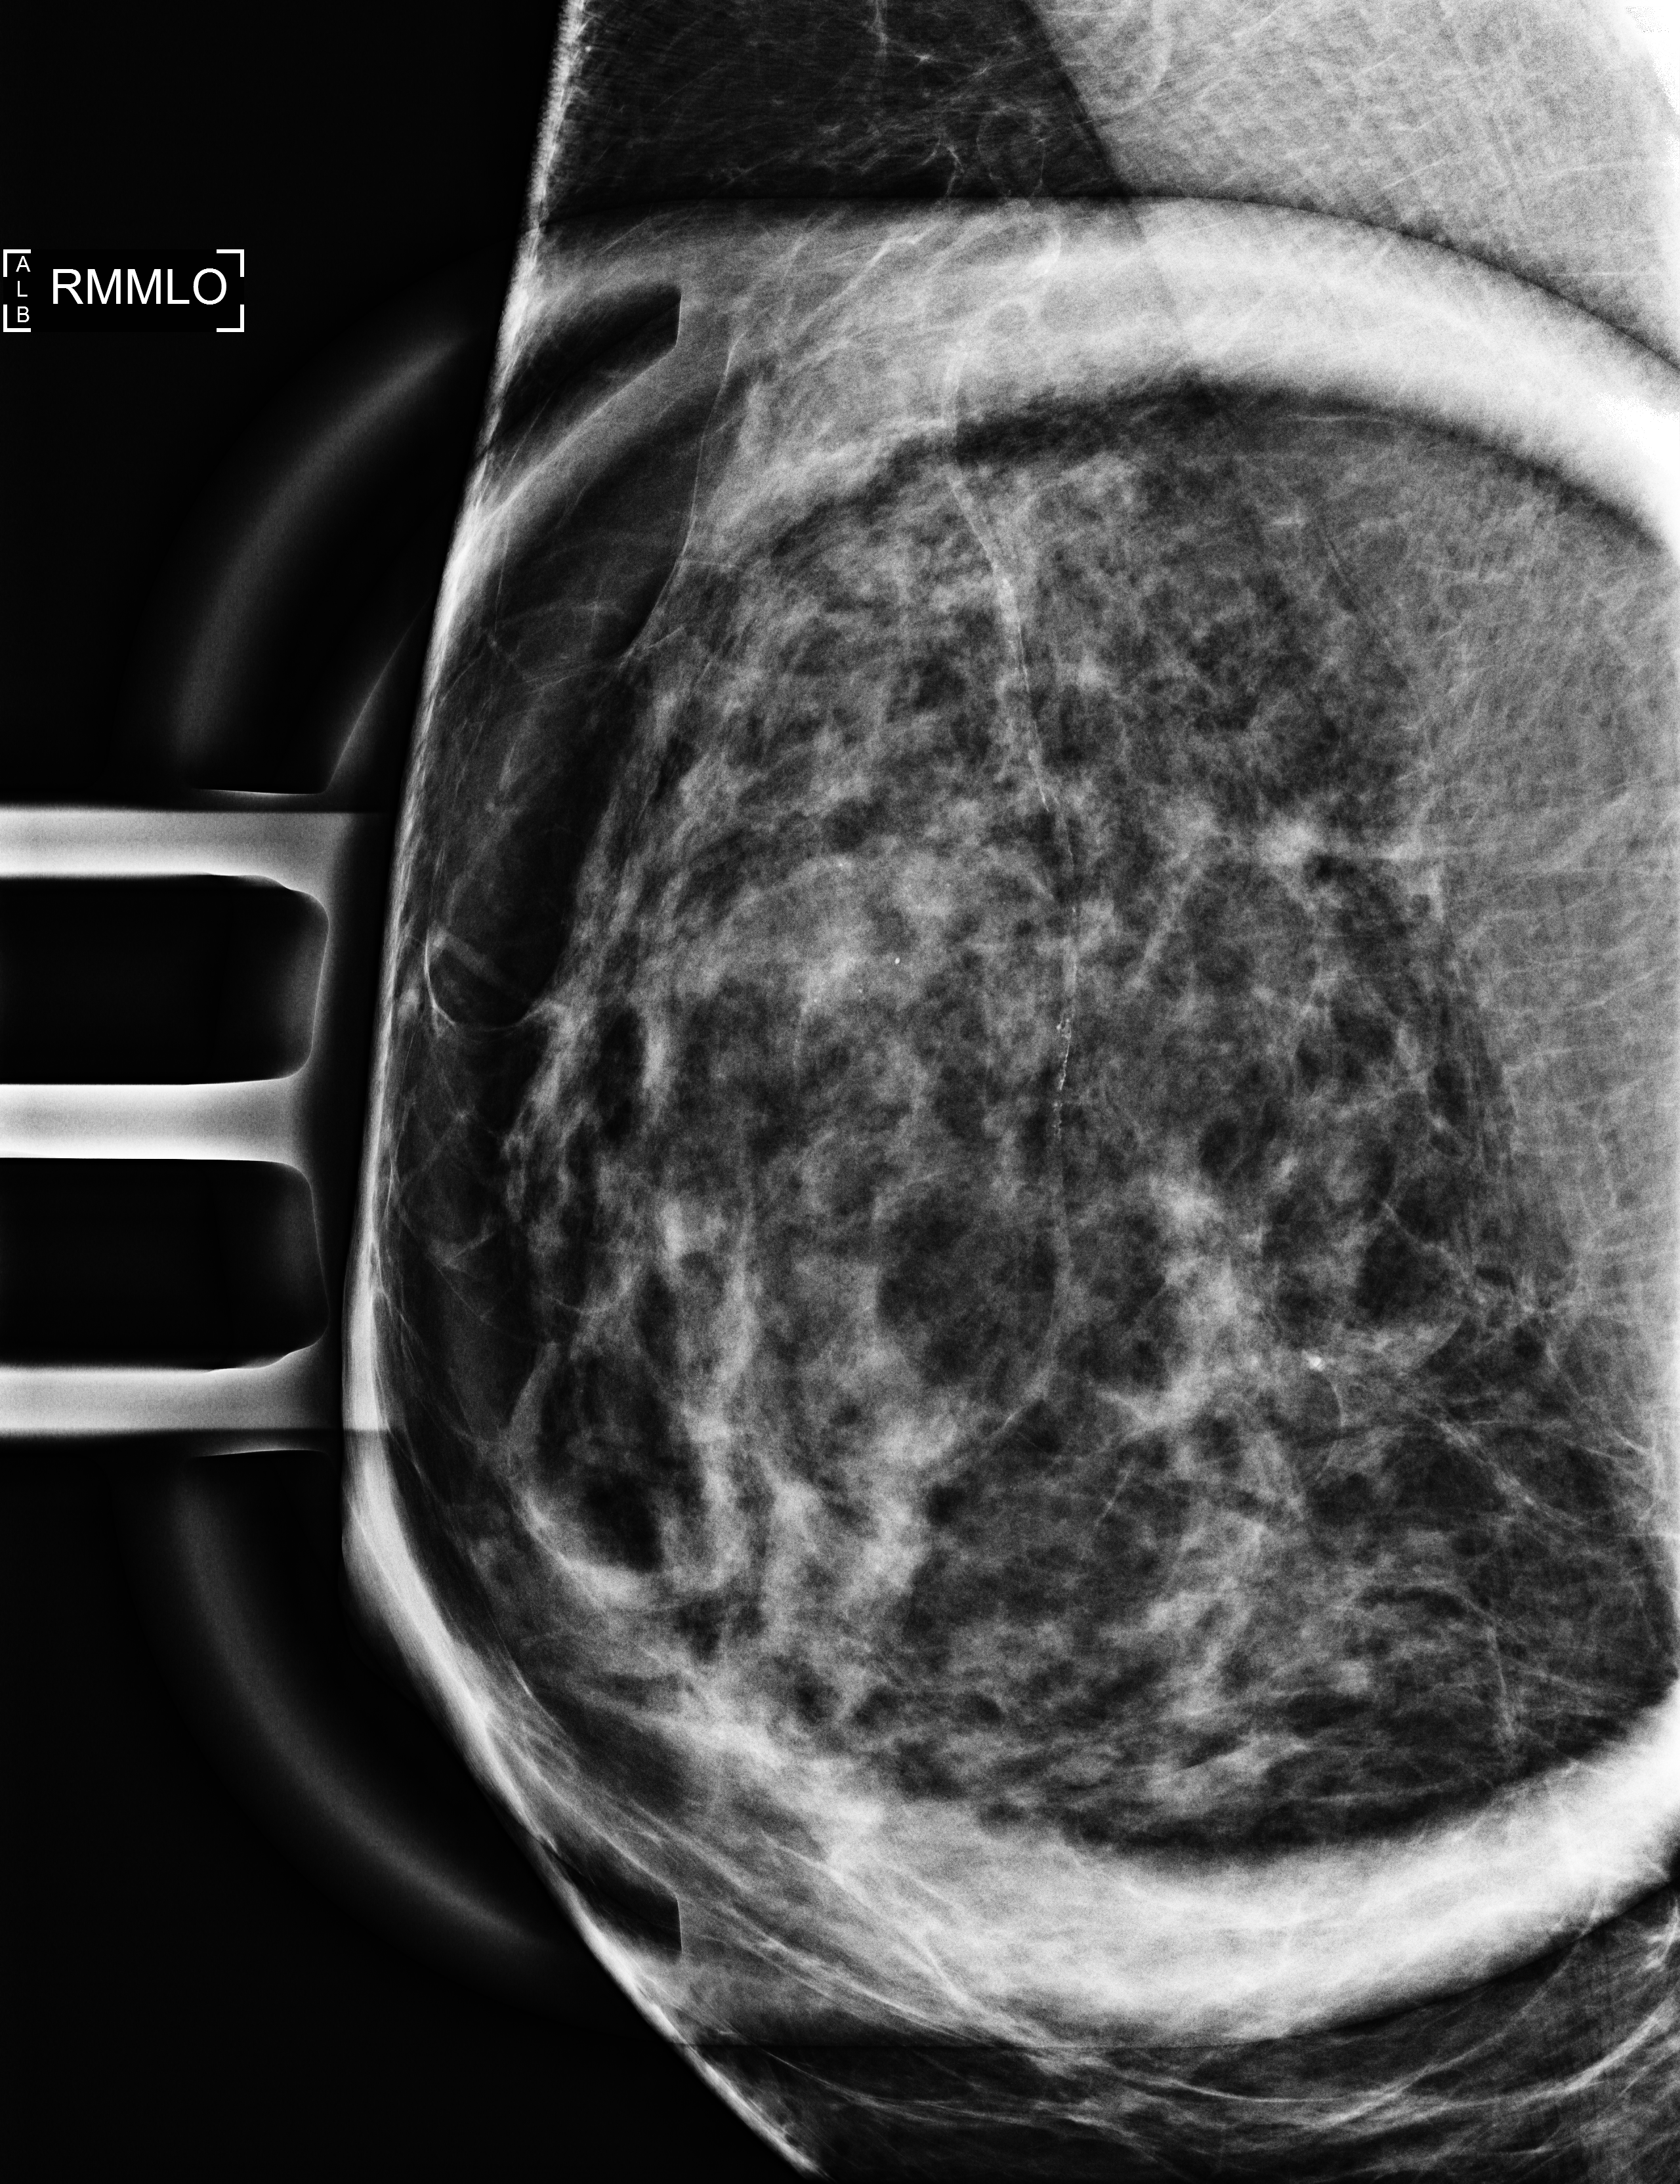
Additional (diagnostic) view; compressed breast thickness 47 mm. Female patient, age 55 years.
Image type: full-field digital mammogram. Breast: right. Projection: MLO view, magnification.